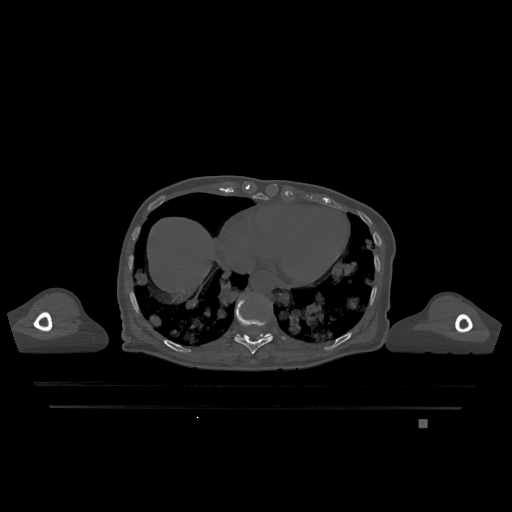
CT including the spine, one axial slice. Slice 629 of 1317 in the series (ordered by position). Bone window (W 1800 / L 400 HU). 512 × 512 image matrix, field of view 500 × 500 mm. Patient: female, 74 years. From the clinical record (not read from this slice): primary cancer: lung.
Outlined on this slice (semi-automatic segmentation, software-assisted and operator-edited):
- T10 vertebra: bounding box (x1, y1, x2, y2) in pixels: (234, 301, 273, 354)
- T11 vertebra: (237, 333, 271, 338)